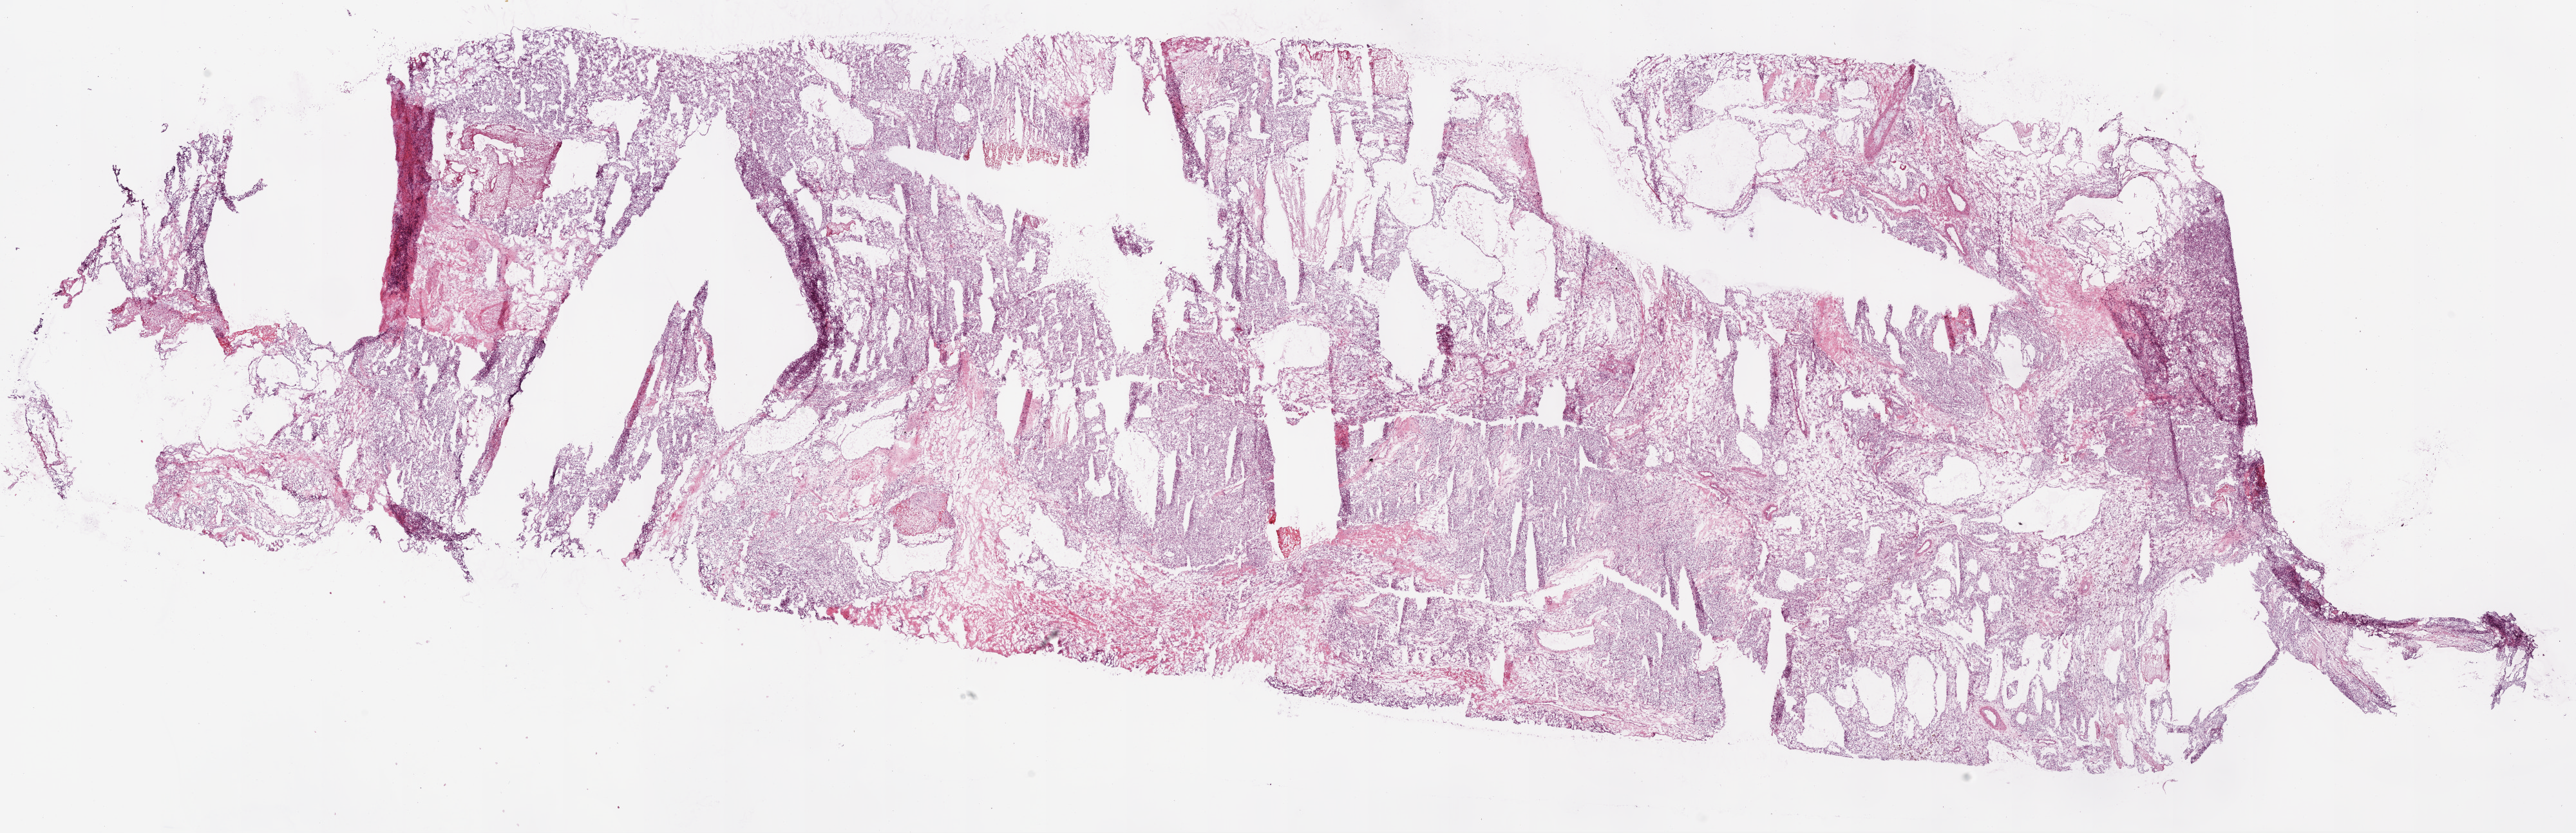
Whole-slide histology image, H&E-stained — shown as a low-resolution overview of the whole scanned area (about 32.1 x 10.4 mm). Frozen section. Primary tumour sample from the kidney. Patient: male, age at initial diagnosis 47 years. Histologic grade: G2 (moderately differentiated). Slide review estimates, as recorded: tumour cells 90%, tumour nuclei 85%, normal cells 0%, stromal cells 10%, necrosis 0%.
Laterality: right. AJCC pathologic stage: II (7th edition). Pathologic diagnosis: Clear cell adenocarcinoma, NOS.